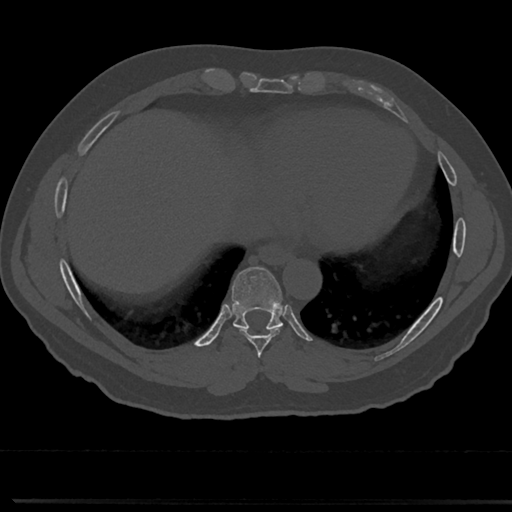
CT including the spine, one axial slice. Position 330 of 817 along the scan axis. 120 kVp. Bone window (W 1800 / L 400 HU). 0.5 mm slice thickness. 512 × 512 image matrix, field of view 355 × 355 mm. Male patient, age 61 years. From the clinical record (not read from this slice): primary cancer: prostate.
Annotated regions visible in this slice (semi-automatic segmentation, software-assisted and operator-edited):
- T7 vertebra: box from (x=258, y=349) to (x=266, y=376) px
- T8 vertebra: (x=211, y=270)–(x=310, y=357)